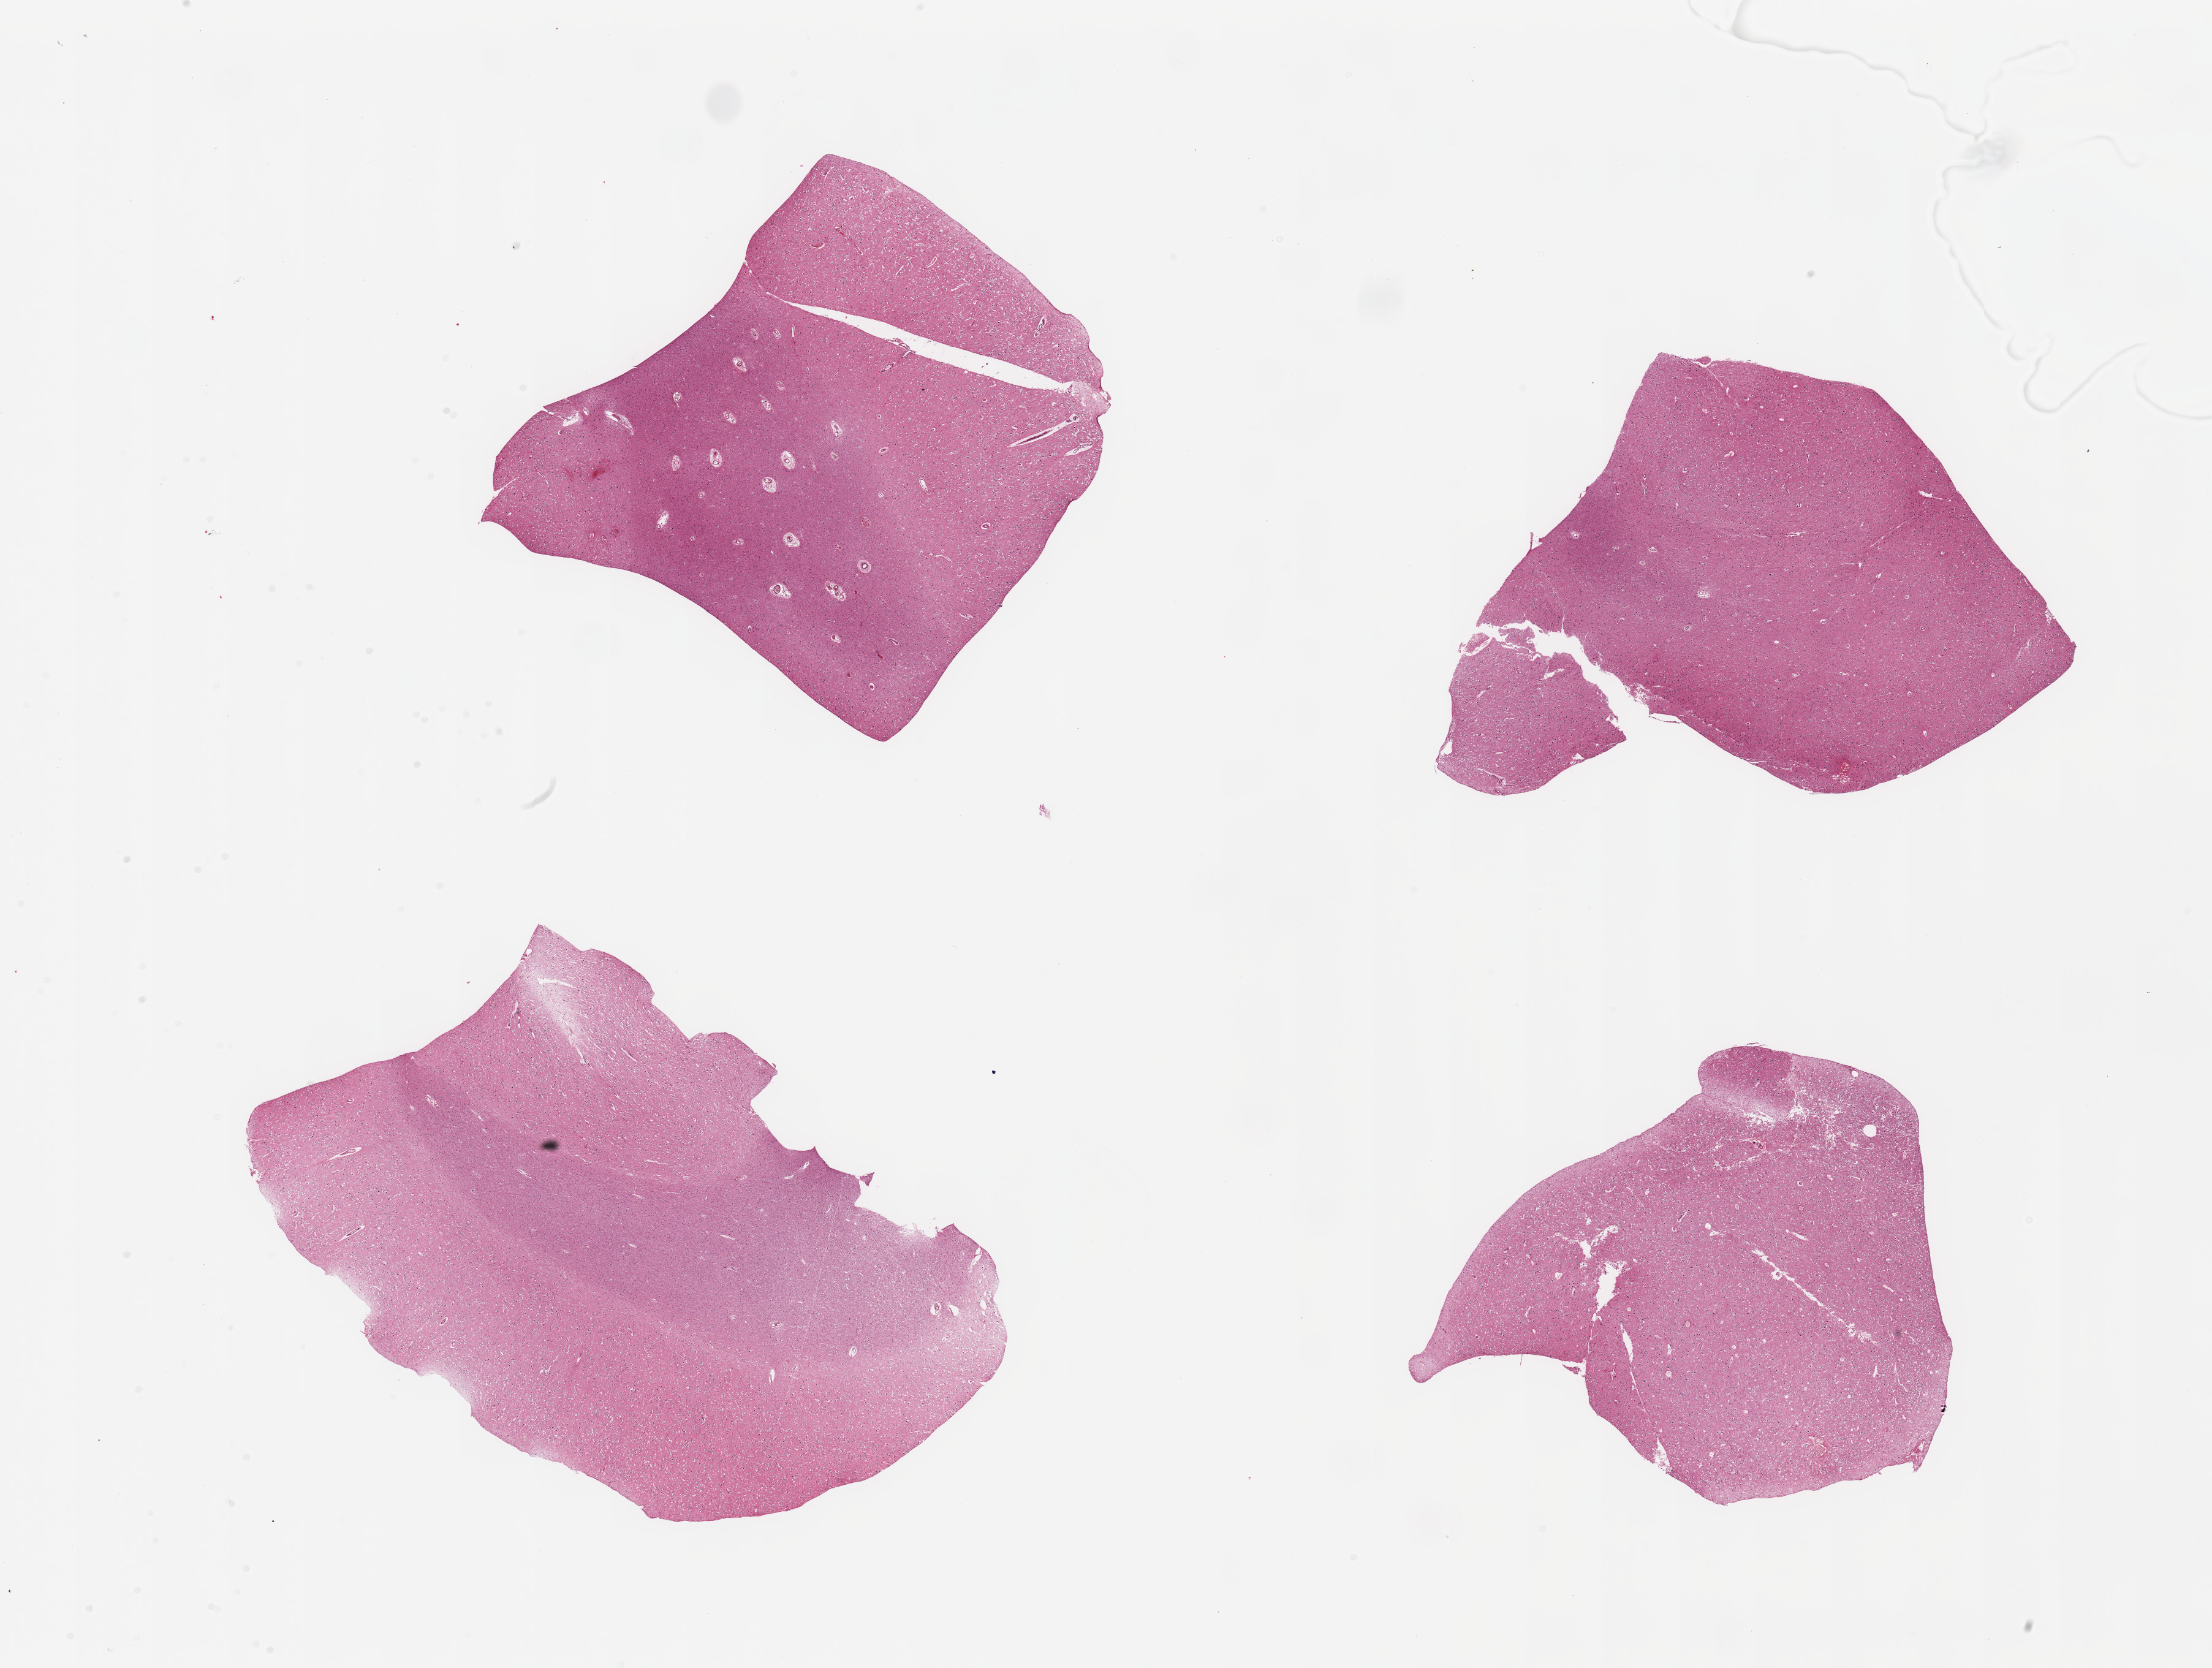
Hematoxylin and eosin (H&E) whole-slide image — shown as a low-resolution overview of the whole scanned area (about 28.5 x 21.5 mm), PAXgene-fixed paraffin-embedded (PFPE) section, target tissue: cerebral cortex, tissue donor sample. Donor: male.
Pathologist's review note for this sample: 4 pieces, no abnormalities.